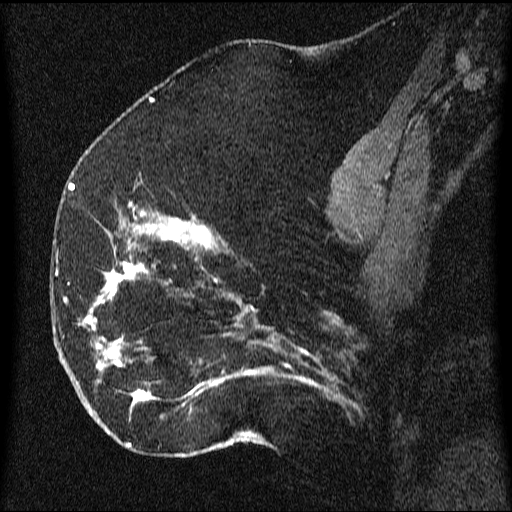
Breast MRI (dynamic contrast-enhanced), one sagittal slice; position 28 of 64 along the scan axis; dynamic contrast-enhanced series, image 2 of 3 at this slice position (ordered by acquisition); 1.5 T; TE 4.2 ms, TR 9.1 ms; 2.2 mm slice thickness; 512 × 512 image matrix, field of view 180 × 180 mm. Female patient, age 52 years.
Outlined on this slice (semi-automatic segmentation, software-assisted and operator-edited):
- analysis volume of interest (the breast-tissue region the enhancement analysis was run in; not a lesion): bounding box [x1, y1, x2, y2] px = [61, 203, 350, 438]
- tumour enhancement mask (voxels above the 70 % enhancement threshold inside the analysis volume of interest): [64, 203, 327, 422]